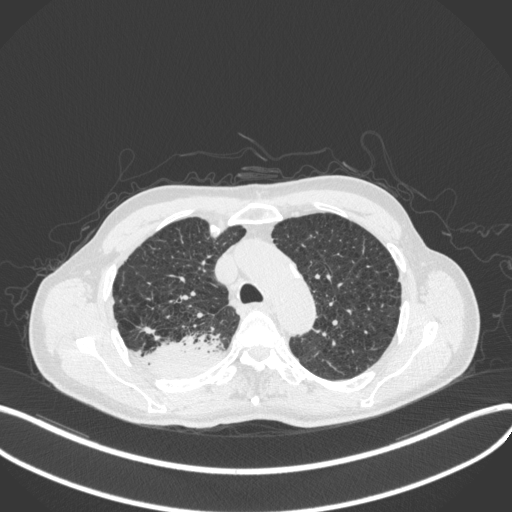
Chest CT, one axial slice. Position 331 of 423 along the scan axis. Lung window (W 1500 / L -600 HU). 1 mm slice thickness. 512 × 512 image matrix. Patient: male, 79 years. From the clinical record (not read from this slice): clinical TNM (as recorded): T3 N0 M0.
Structures marked on this image (rectangle marked by the reading radiologist):
- lung tumour (recorded histology: adenocarcinoma): box from (x=139, y=330) to (x=224, y=377) px